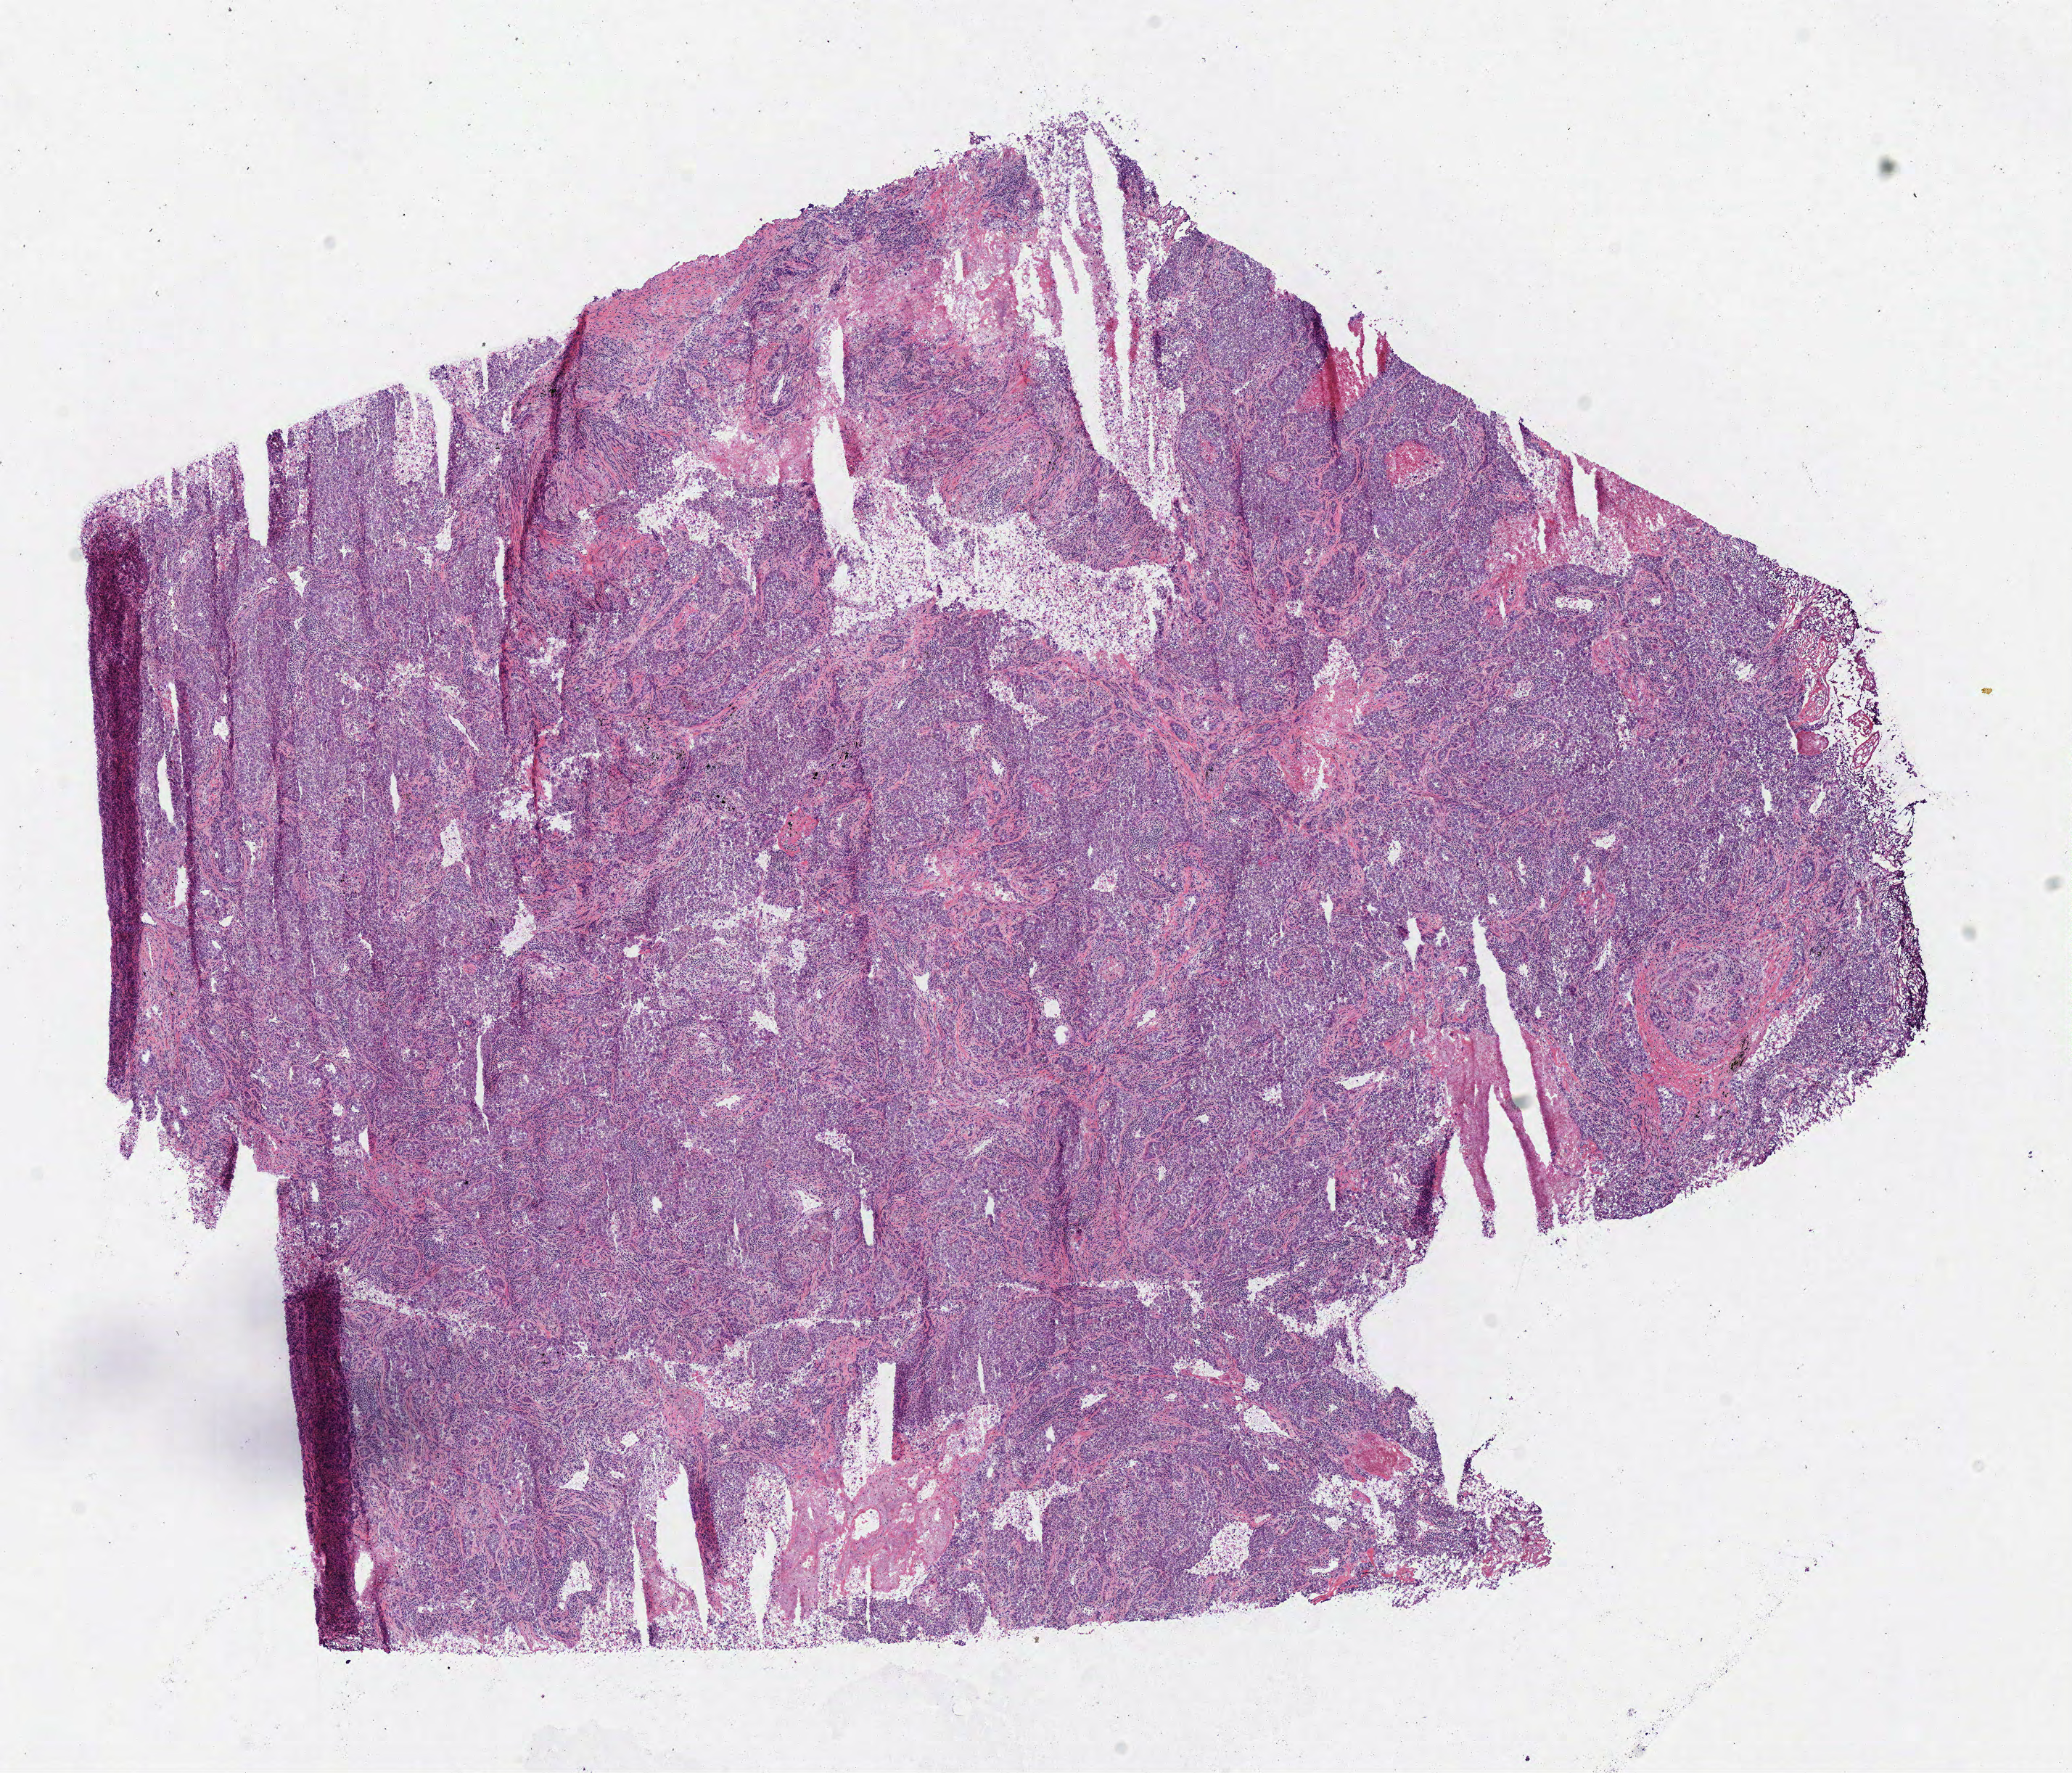
Digitized H&E-stained tissue section (whole slide), whole scanned area (about 11.3 x 9.6 mm) shown as a low-resolution overview. Frozen section from the bottom of the tissue portion. Lung, primary tumour sample. Male patient; age at initial diagnosis 79 years. Slide review estimates, as recorded: tumour cells 89%, tumour nuclei 80%, normal cells 0%, stromal cells 3%, necrosis 8%.
Histologic diagnosis: Squamous cell carcinoma, NOS (overlapping lesion of lung). TNM: T2 N1 M0. AJCC pathologic stage: IIB.